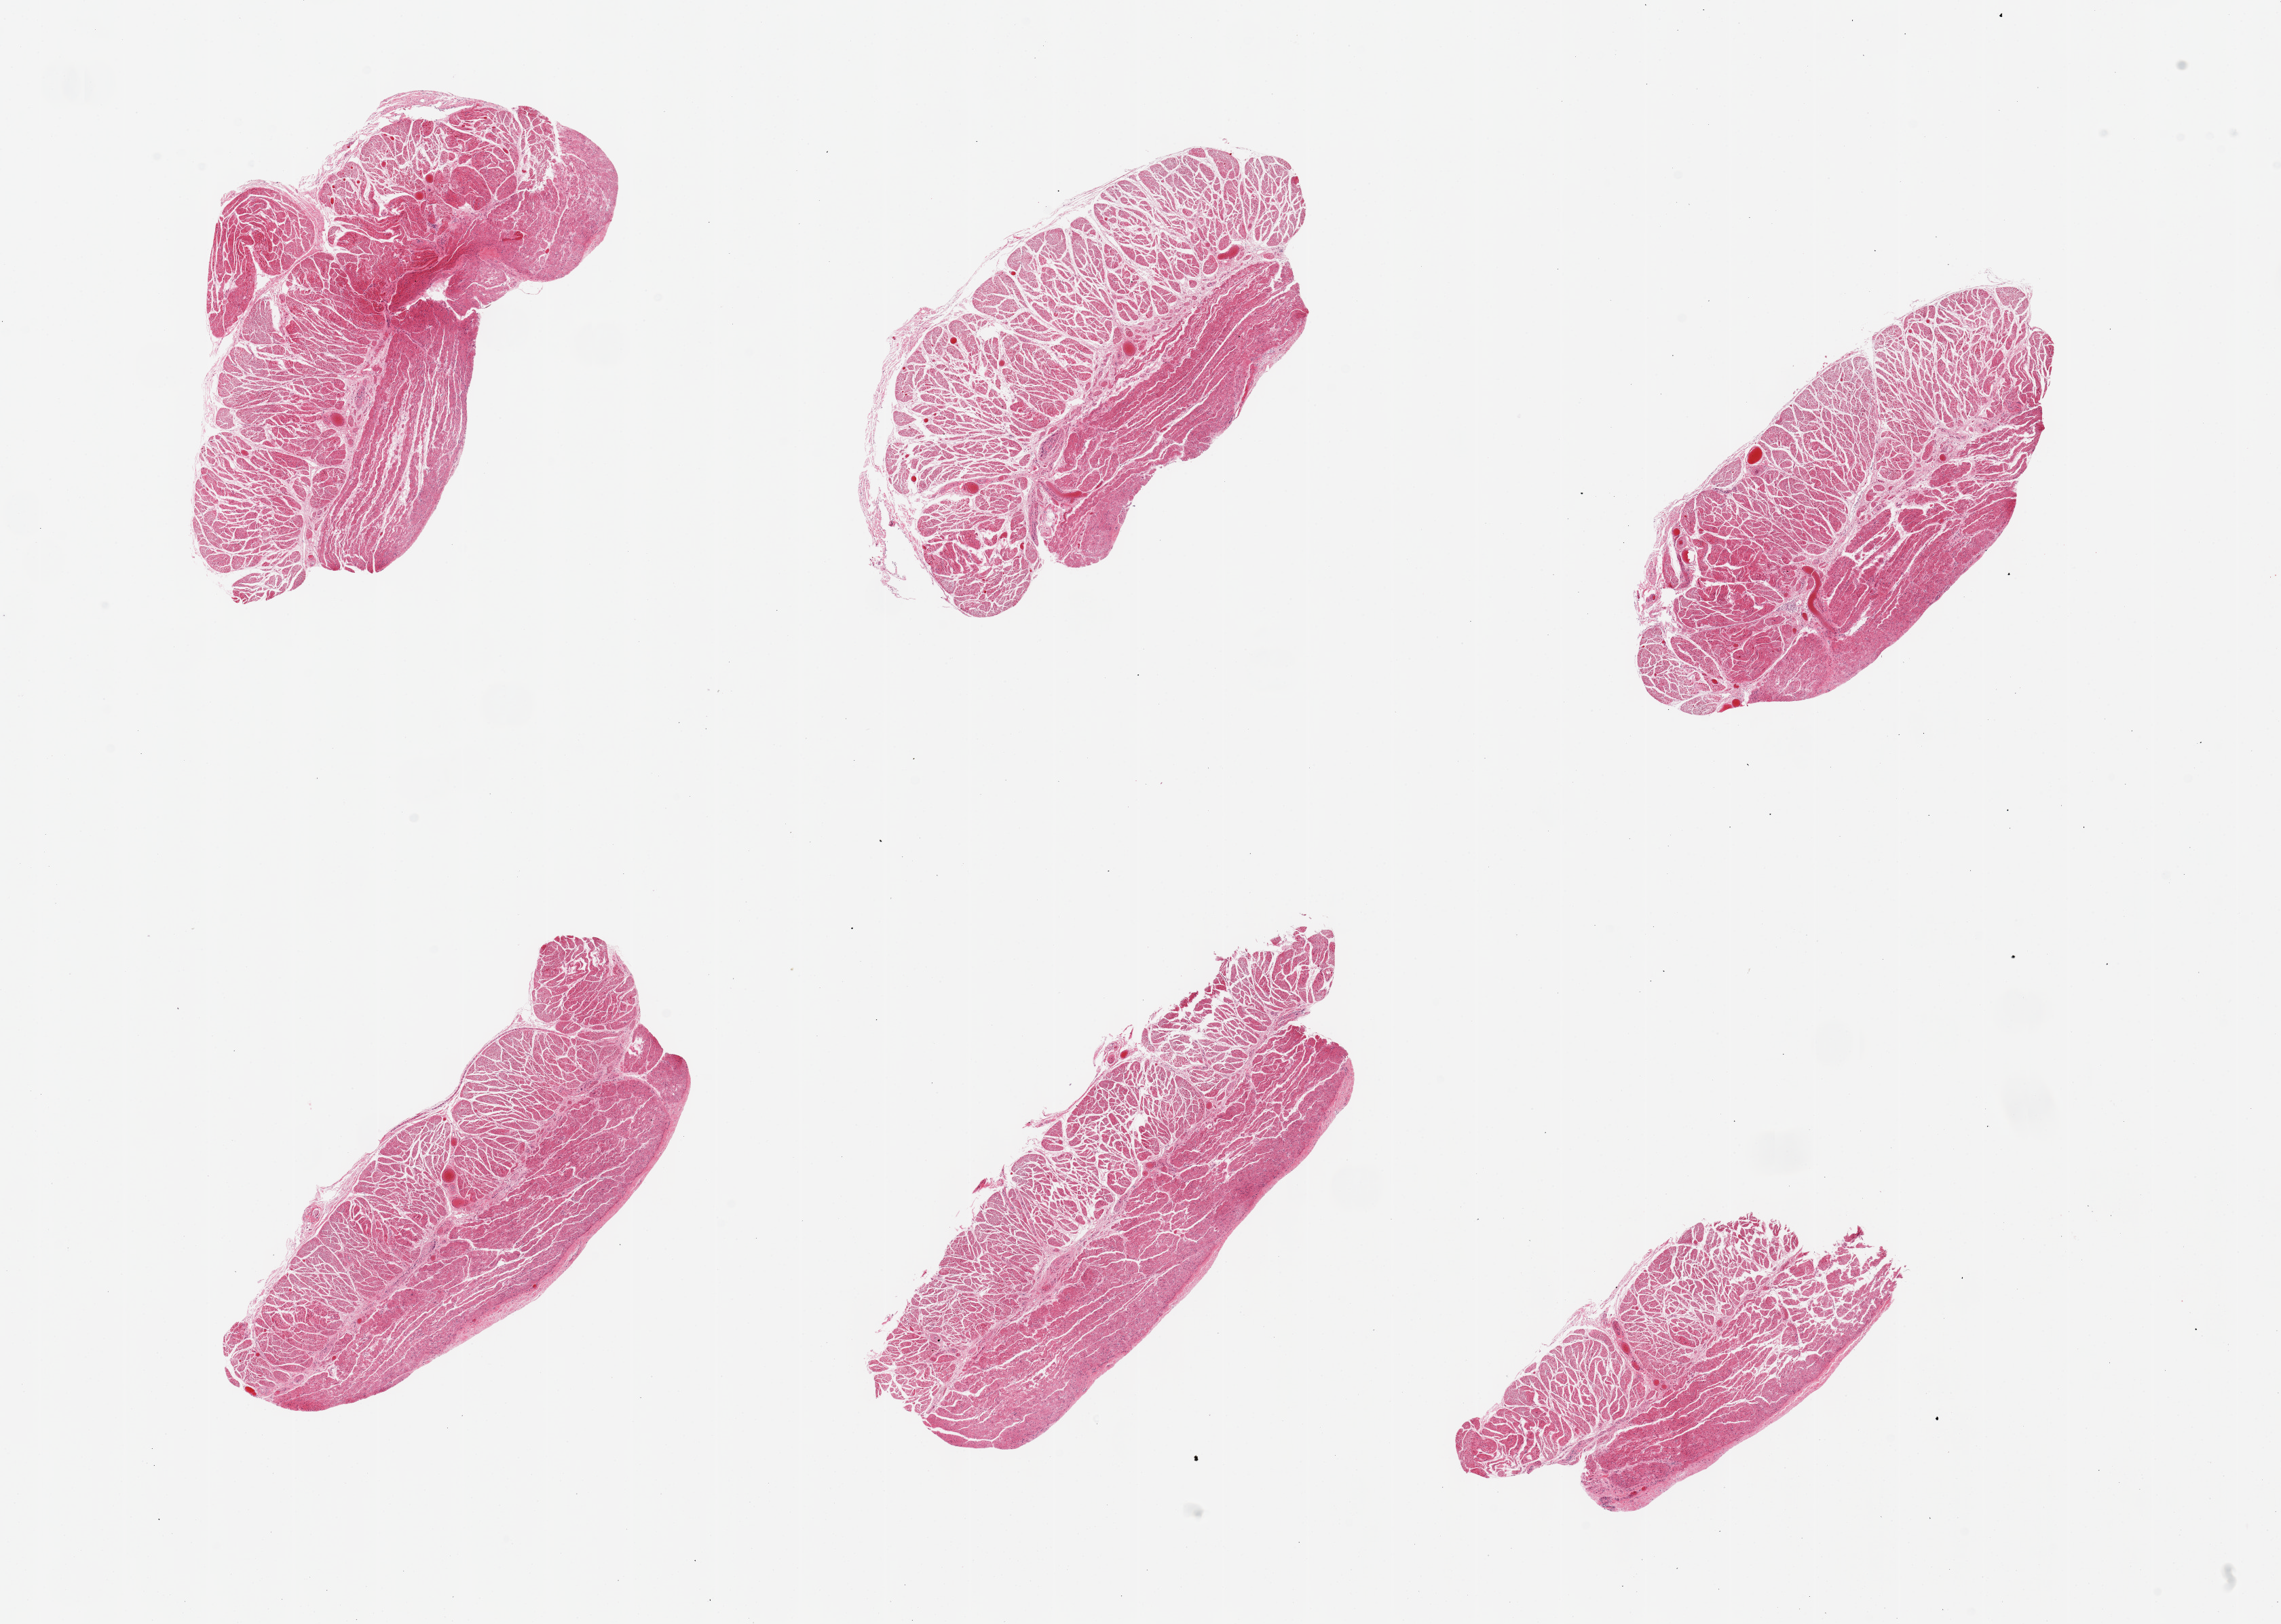
Digitized H&E-stained section, whole scanned area (about 26.6 x 18.9 mm, slide scanned at 20x) shown as a low-resolution overview; PAXgene-fixed, paraffin-embedded tissue; section of esophageal muscle (target tissue); donor tissue sample. Donor: female.
Reviewer comment on this tissue sample: 6 pieces, all muscularis, good specimens.